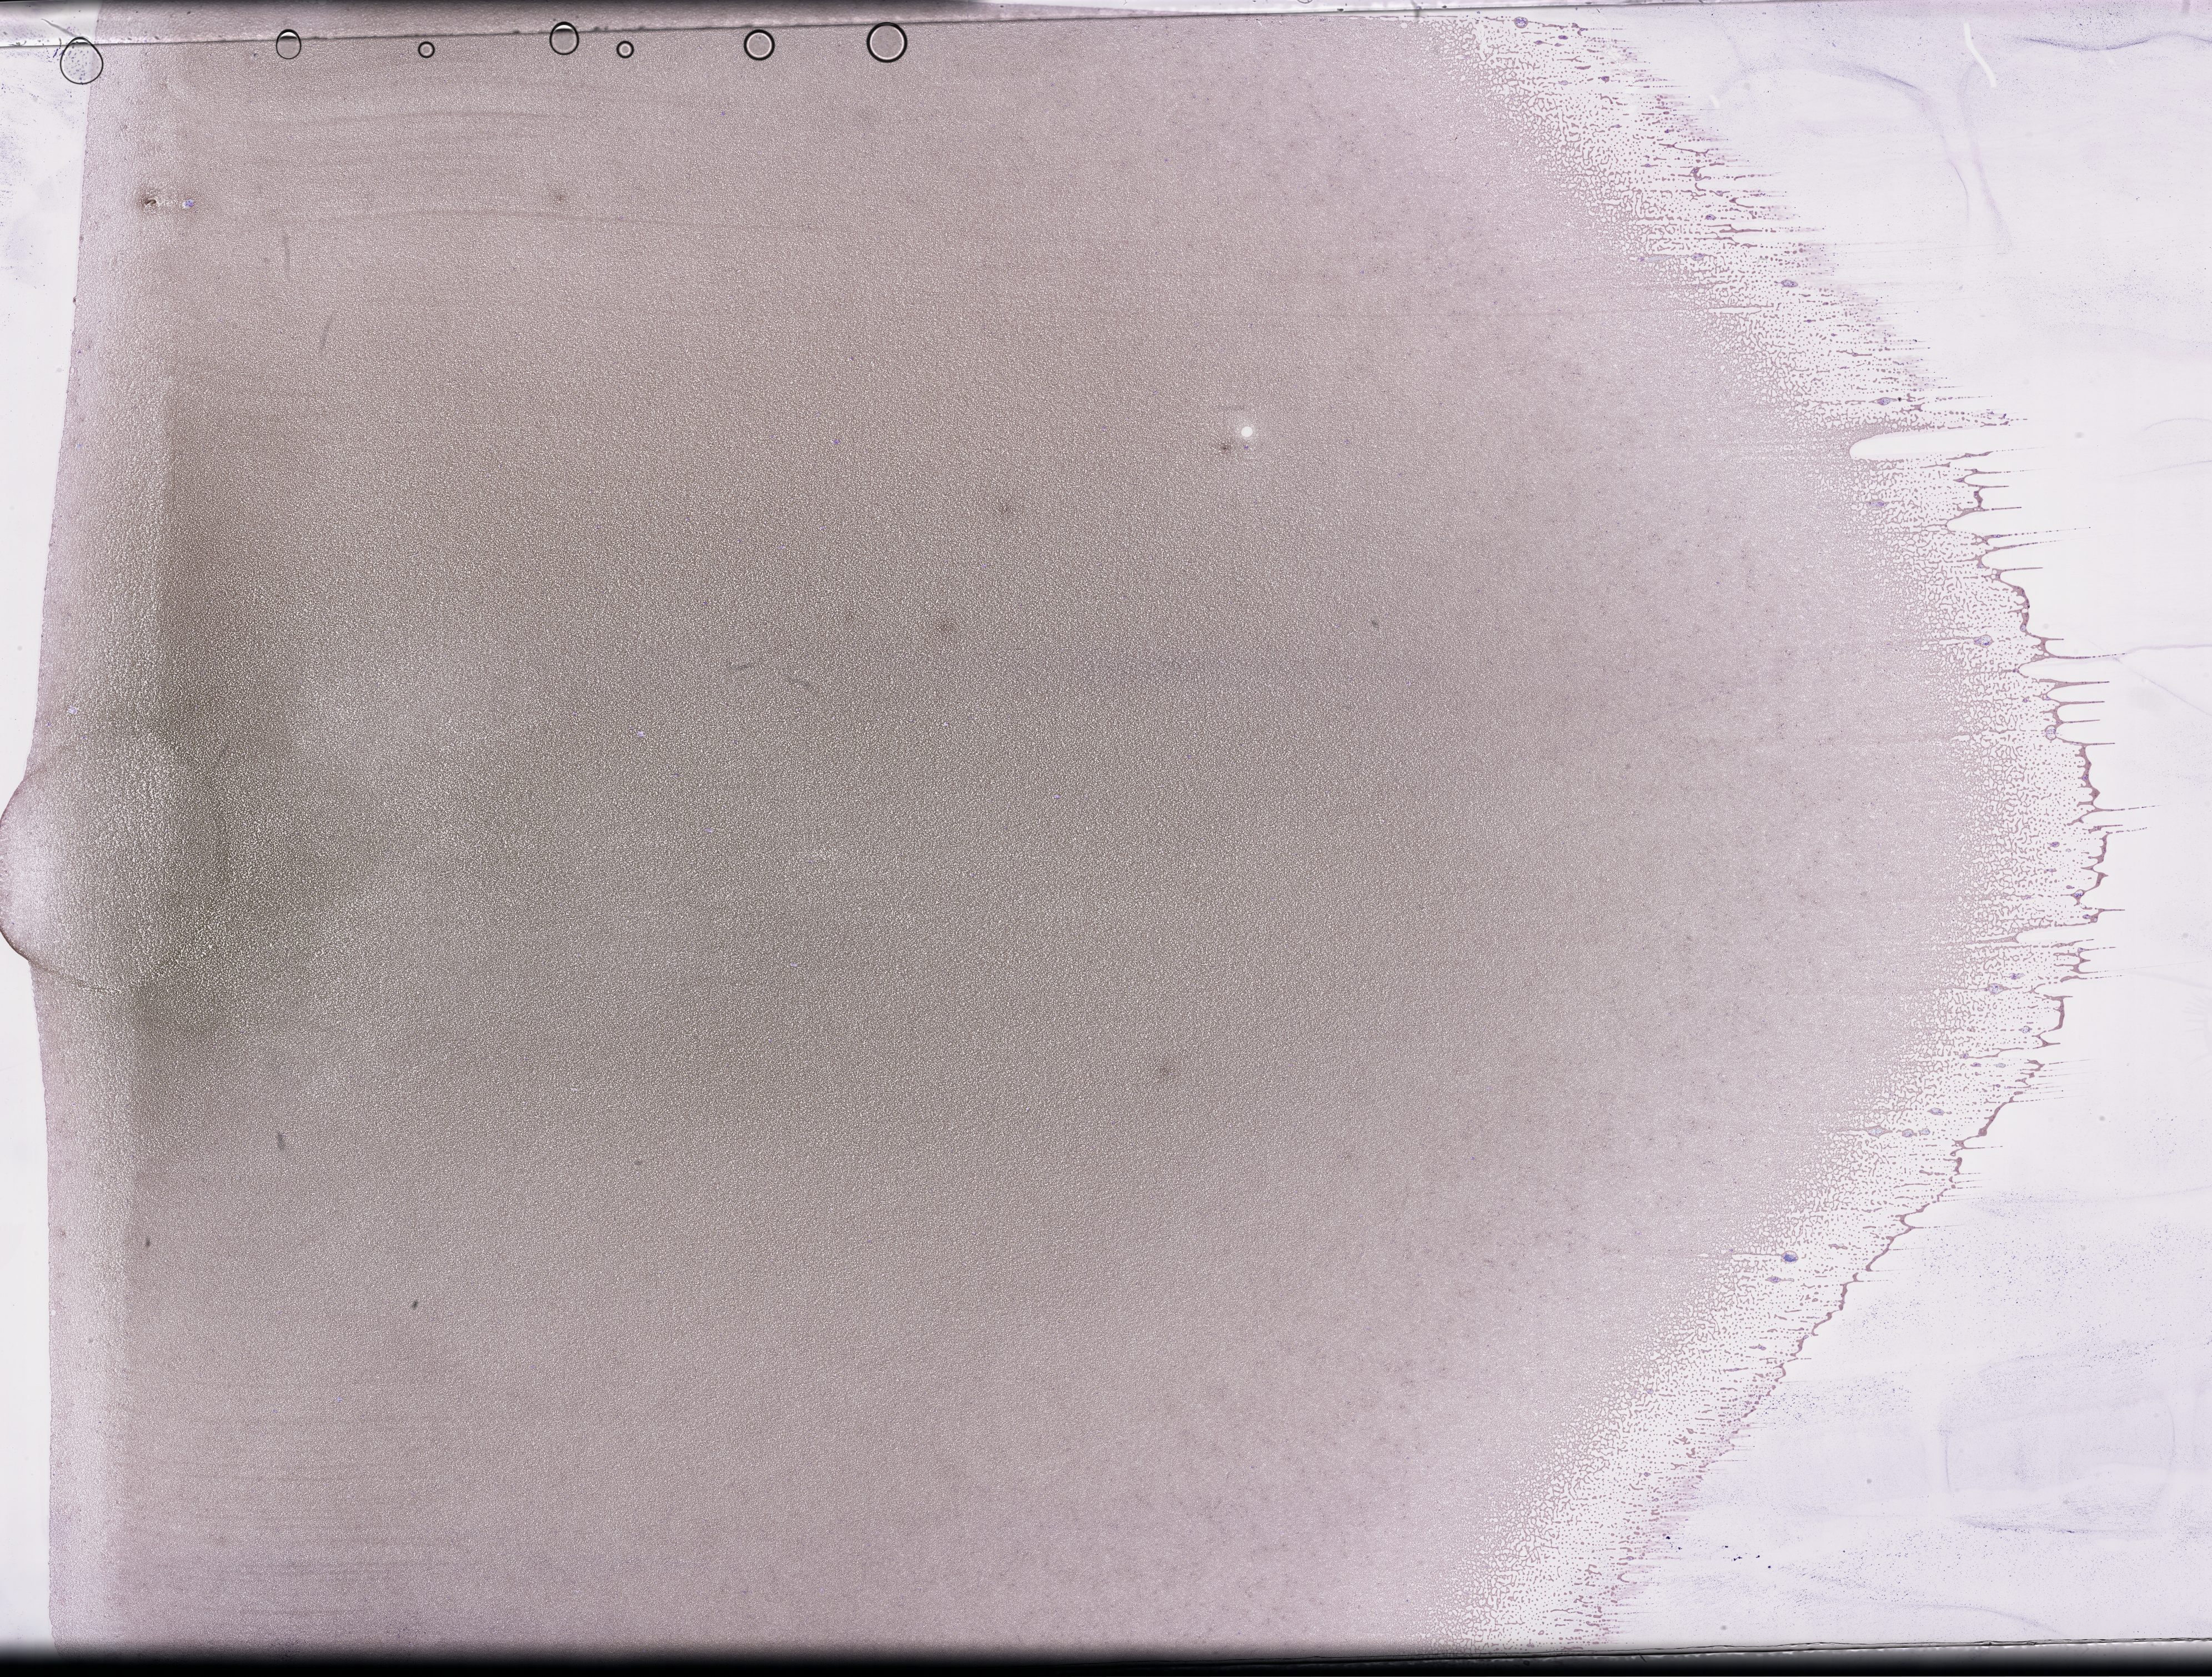
Whole-slide image of a whole blood smear, Wright–Giemsa stain, shown as a low-resolution overview of the whole scanned area (about 32.2 x 24.4 mm); collected on treatment. Male patient.
From a patient with: Plasma Cell Myeloma.